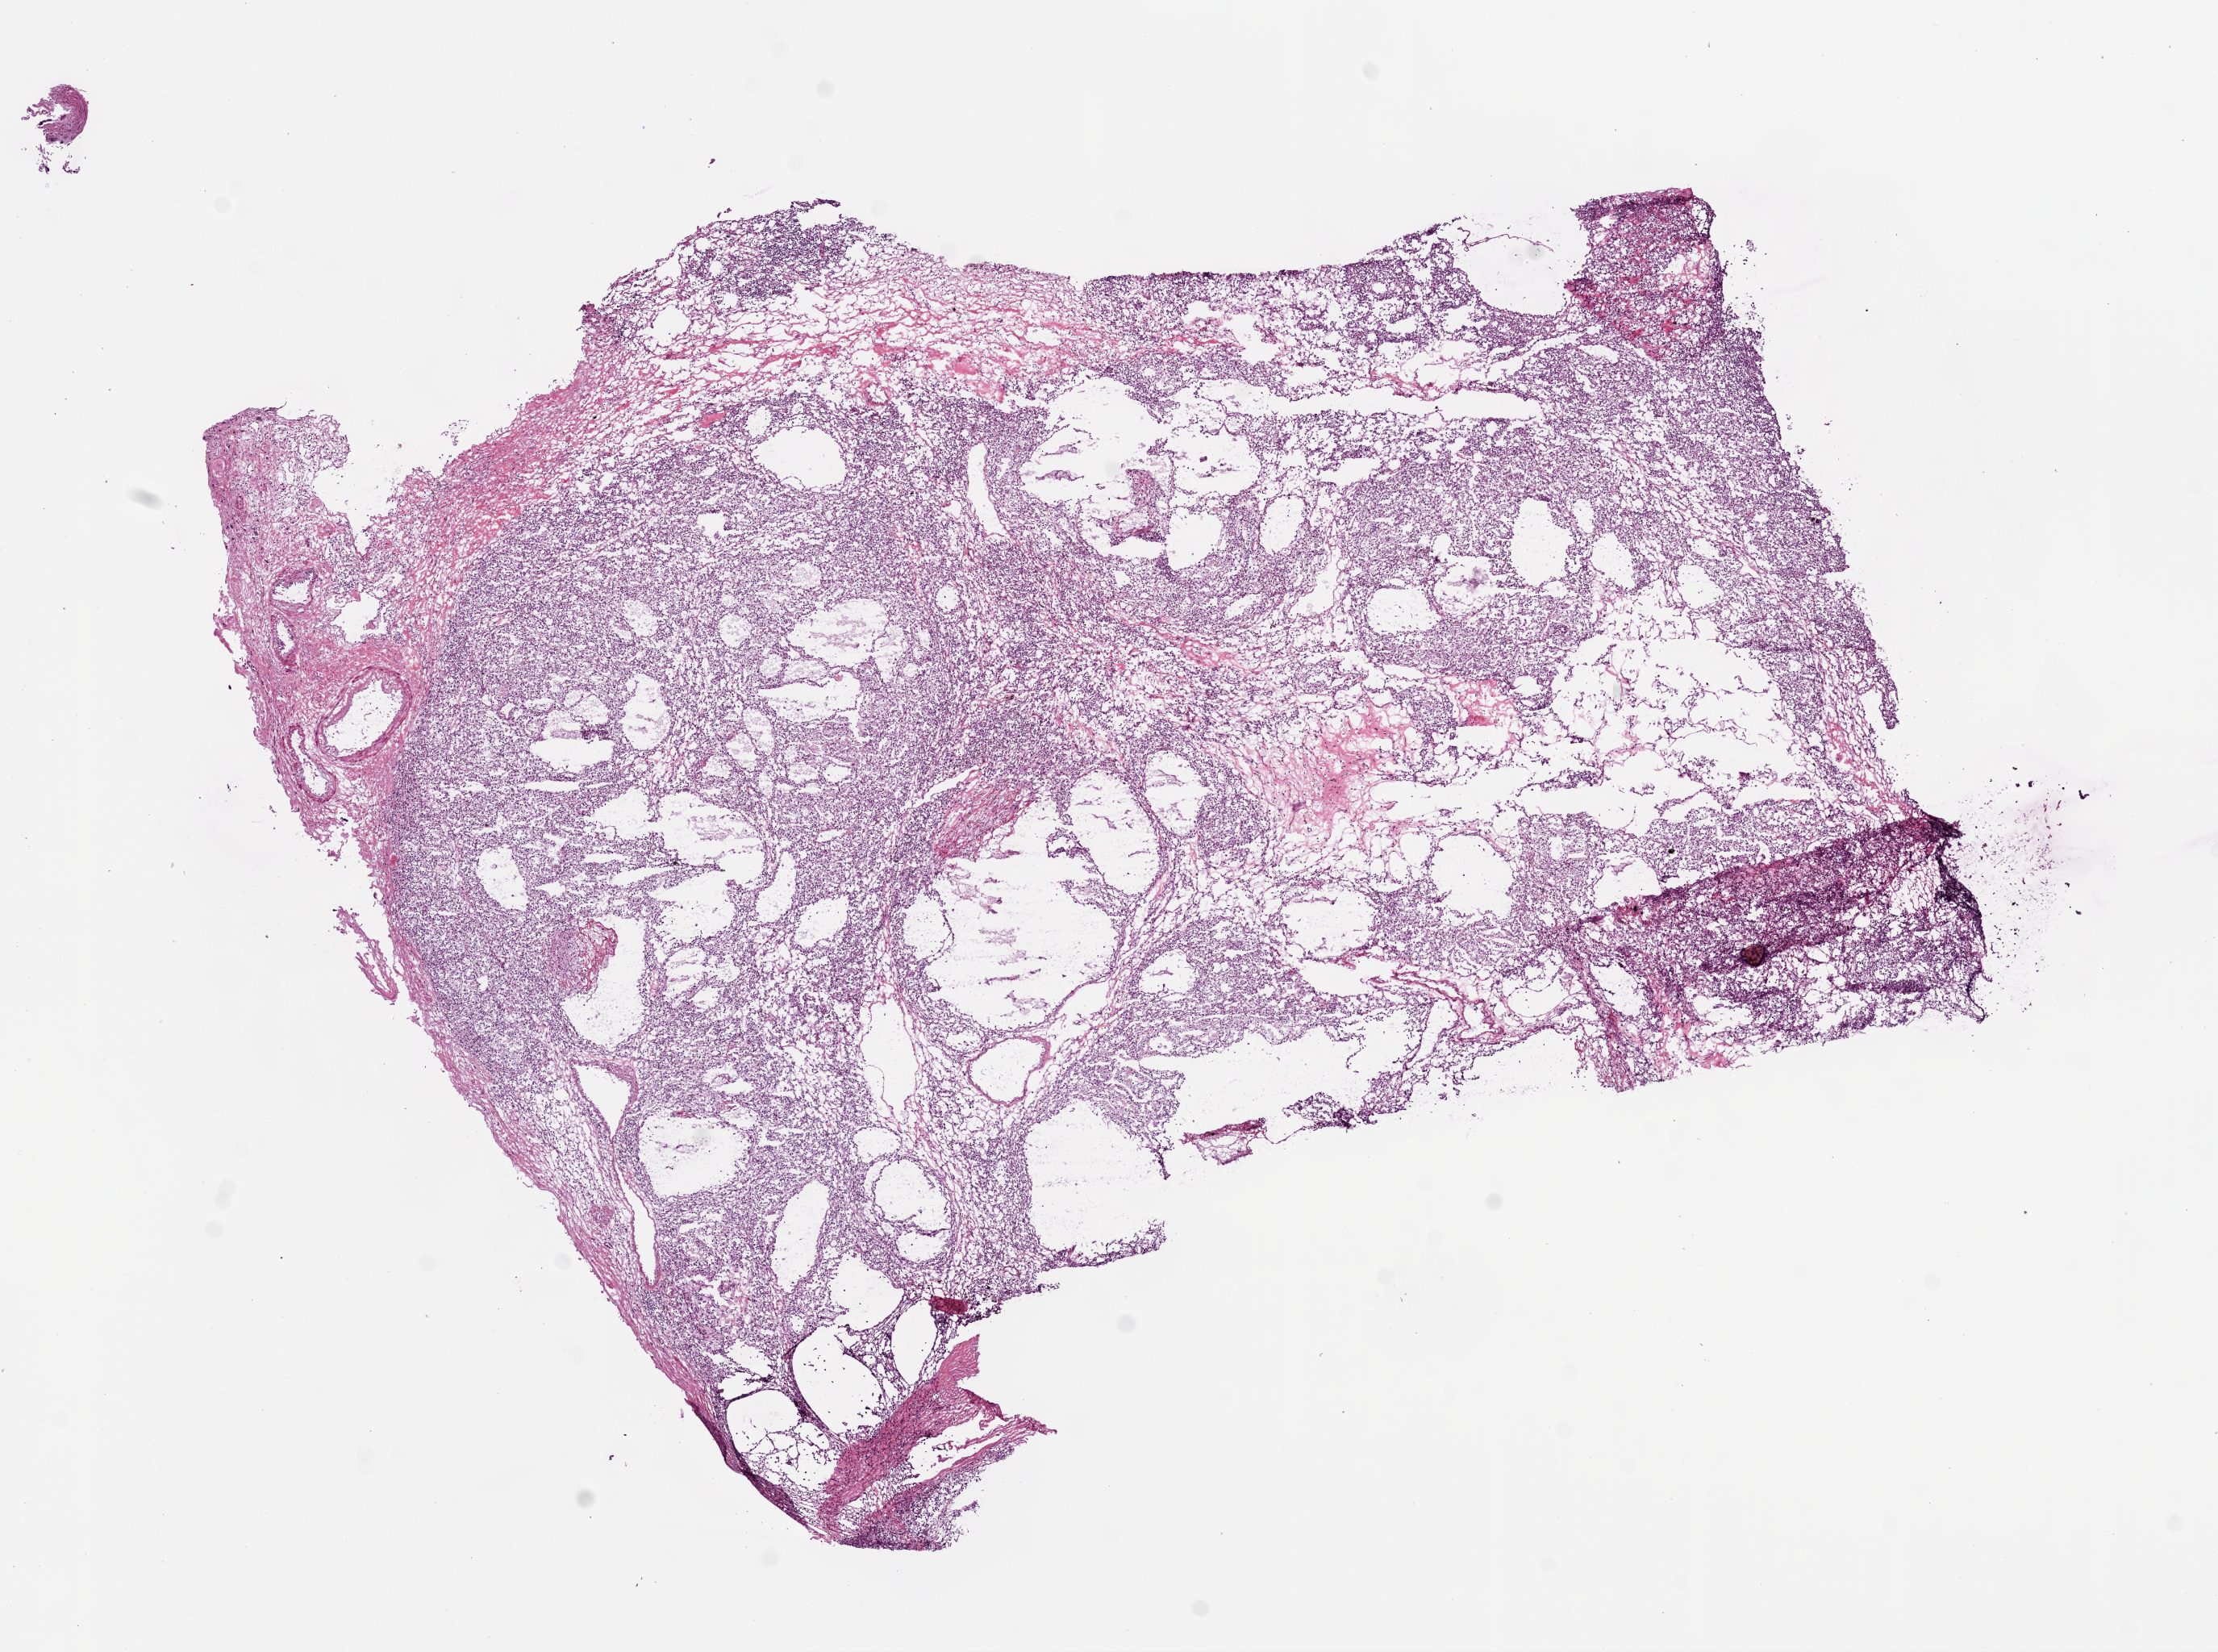
Digitized Hematoxylin and eosin (H&E) stained tissue section (whole slide), shown as a low-resolution overview of the whole scanned area (about 11.0 x 8.2 mm, from a 20x scan). Frozen section from the bottom of the tissue portion. Kidney, primary tumour sample. Female, age 52 years at initial diagnosis.
Pathologic diagnosis: Clear cell adenocarcinoma, NOS.